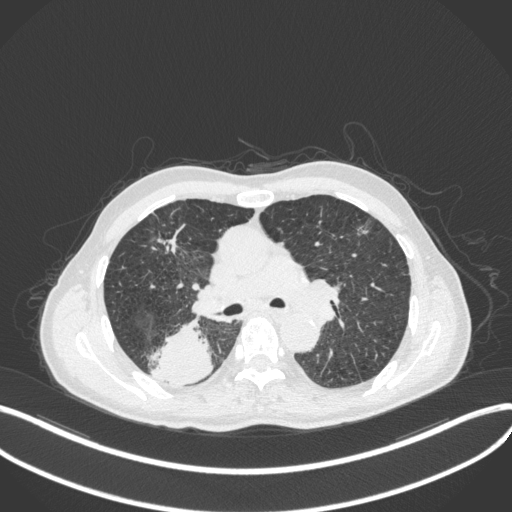
Chest CT, one axial slice; position 280 of 423 along the scan axis; lung window (W 1500 / L -600 HU); 512 × 512 image matrix. Patient: male, 79 years. From the clinical record (not read from this slice): clinical TNM (as recorded): T3 N0 M0.
Structures marked on this image (rectangle marked by the reading radiologist):
- lung tumour (recorded histology: adenocarcinoma): bounding box [x1, y1, x2, y2] px = [146, 314, 215, 386]